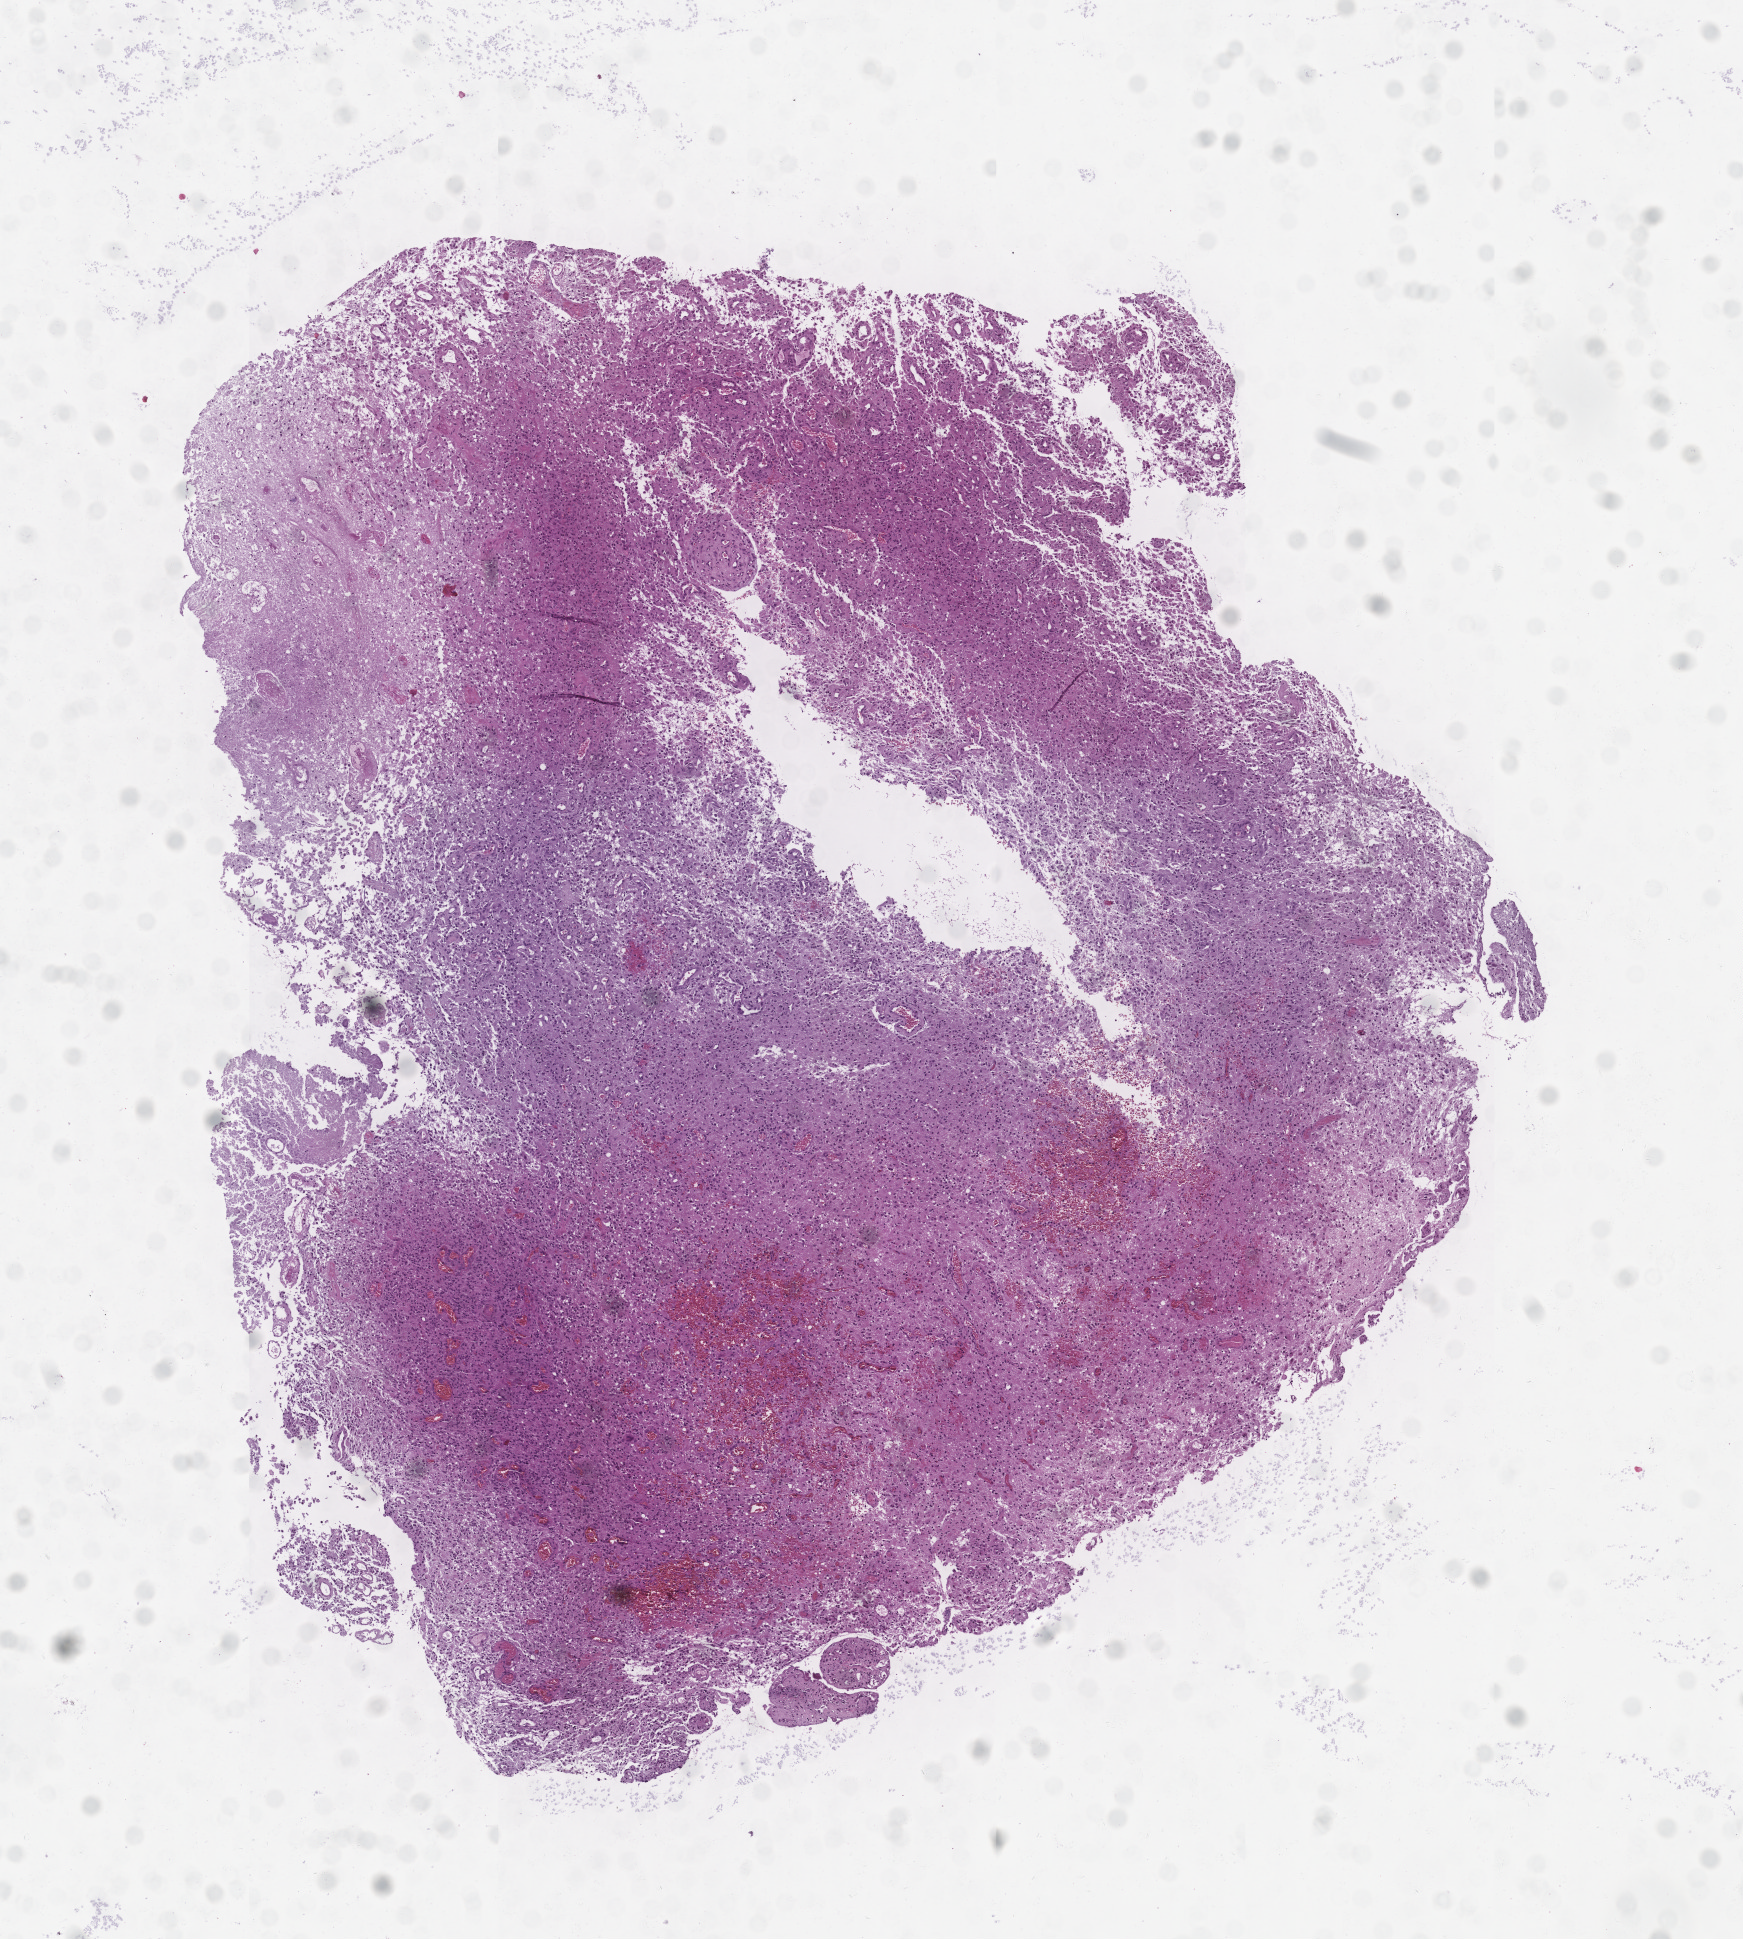
Digitized Hematoxylin and eosin (H&E) stained tissue section (whole slide), a low-resolution overview of the entire scanned area, about 7.0 x 7.8 mm (acquisition: 20x scan). Tumour tissue sample, sampled site: brain. 78-year-old male patient. Pathologist review of this section (percent, as recorded): tumour nuclei 60%, necrosis 30%.
Histologic diagnosis: Glioblastoma.